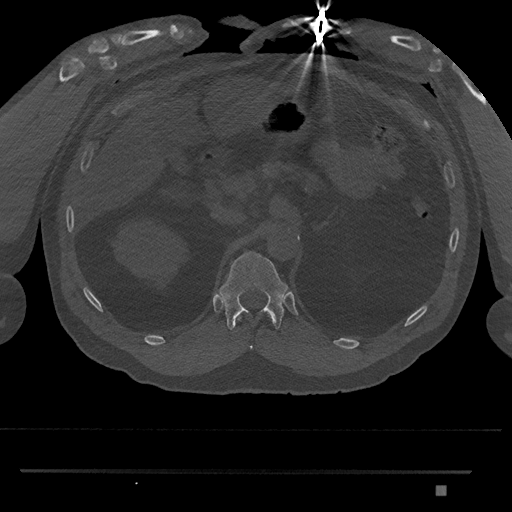
CT including the spine, one axial slice. Position 902 of 1134 along the scan axis. Reconstruction kernel Br40s/3. Bone window (W 1800 / L 400 HU). 0.5 mm slice thickness. 512 × 512 image matrix, field of view 429 × 429 mm. Patient: male, 65 years. From the clinical record (not read from this slice): primary cancer: prostate.
Annotated regions visible in this slice (semi-automatically segmented with operator editing):
- T11 vertebra: bounding box [x1, y1, x2, y2] px = [248, 345, 253, 349]
- T12 vertebra: [219, 251, 288, 331]